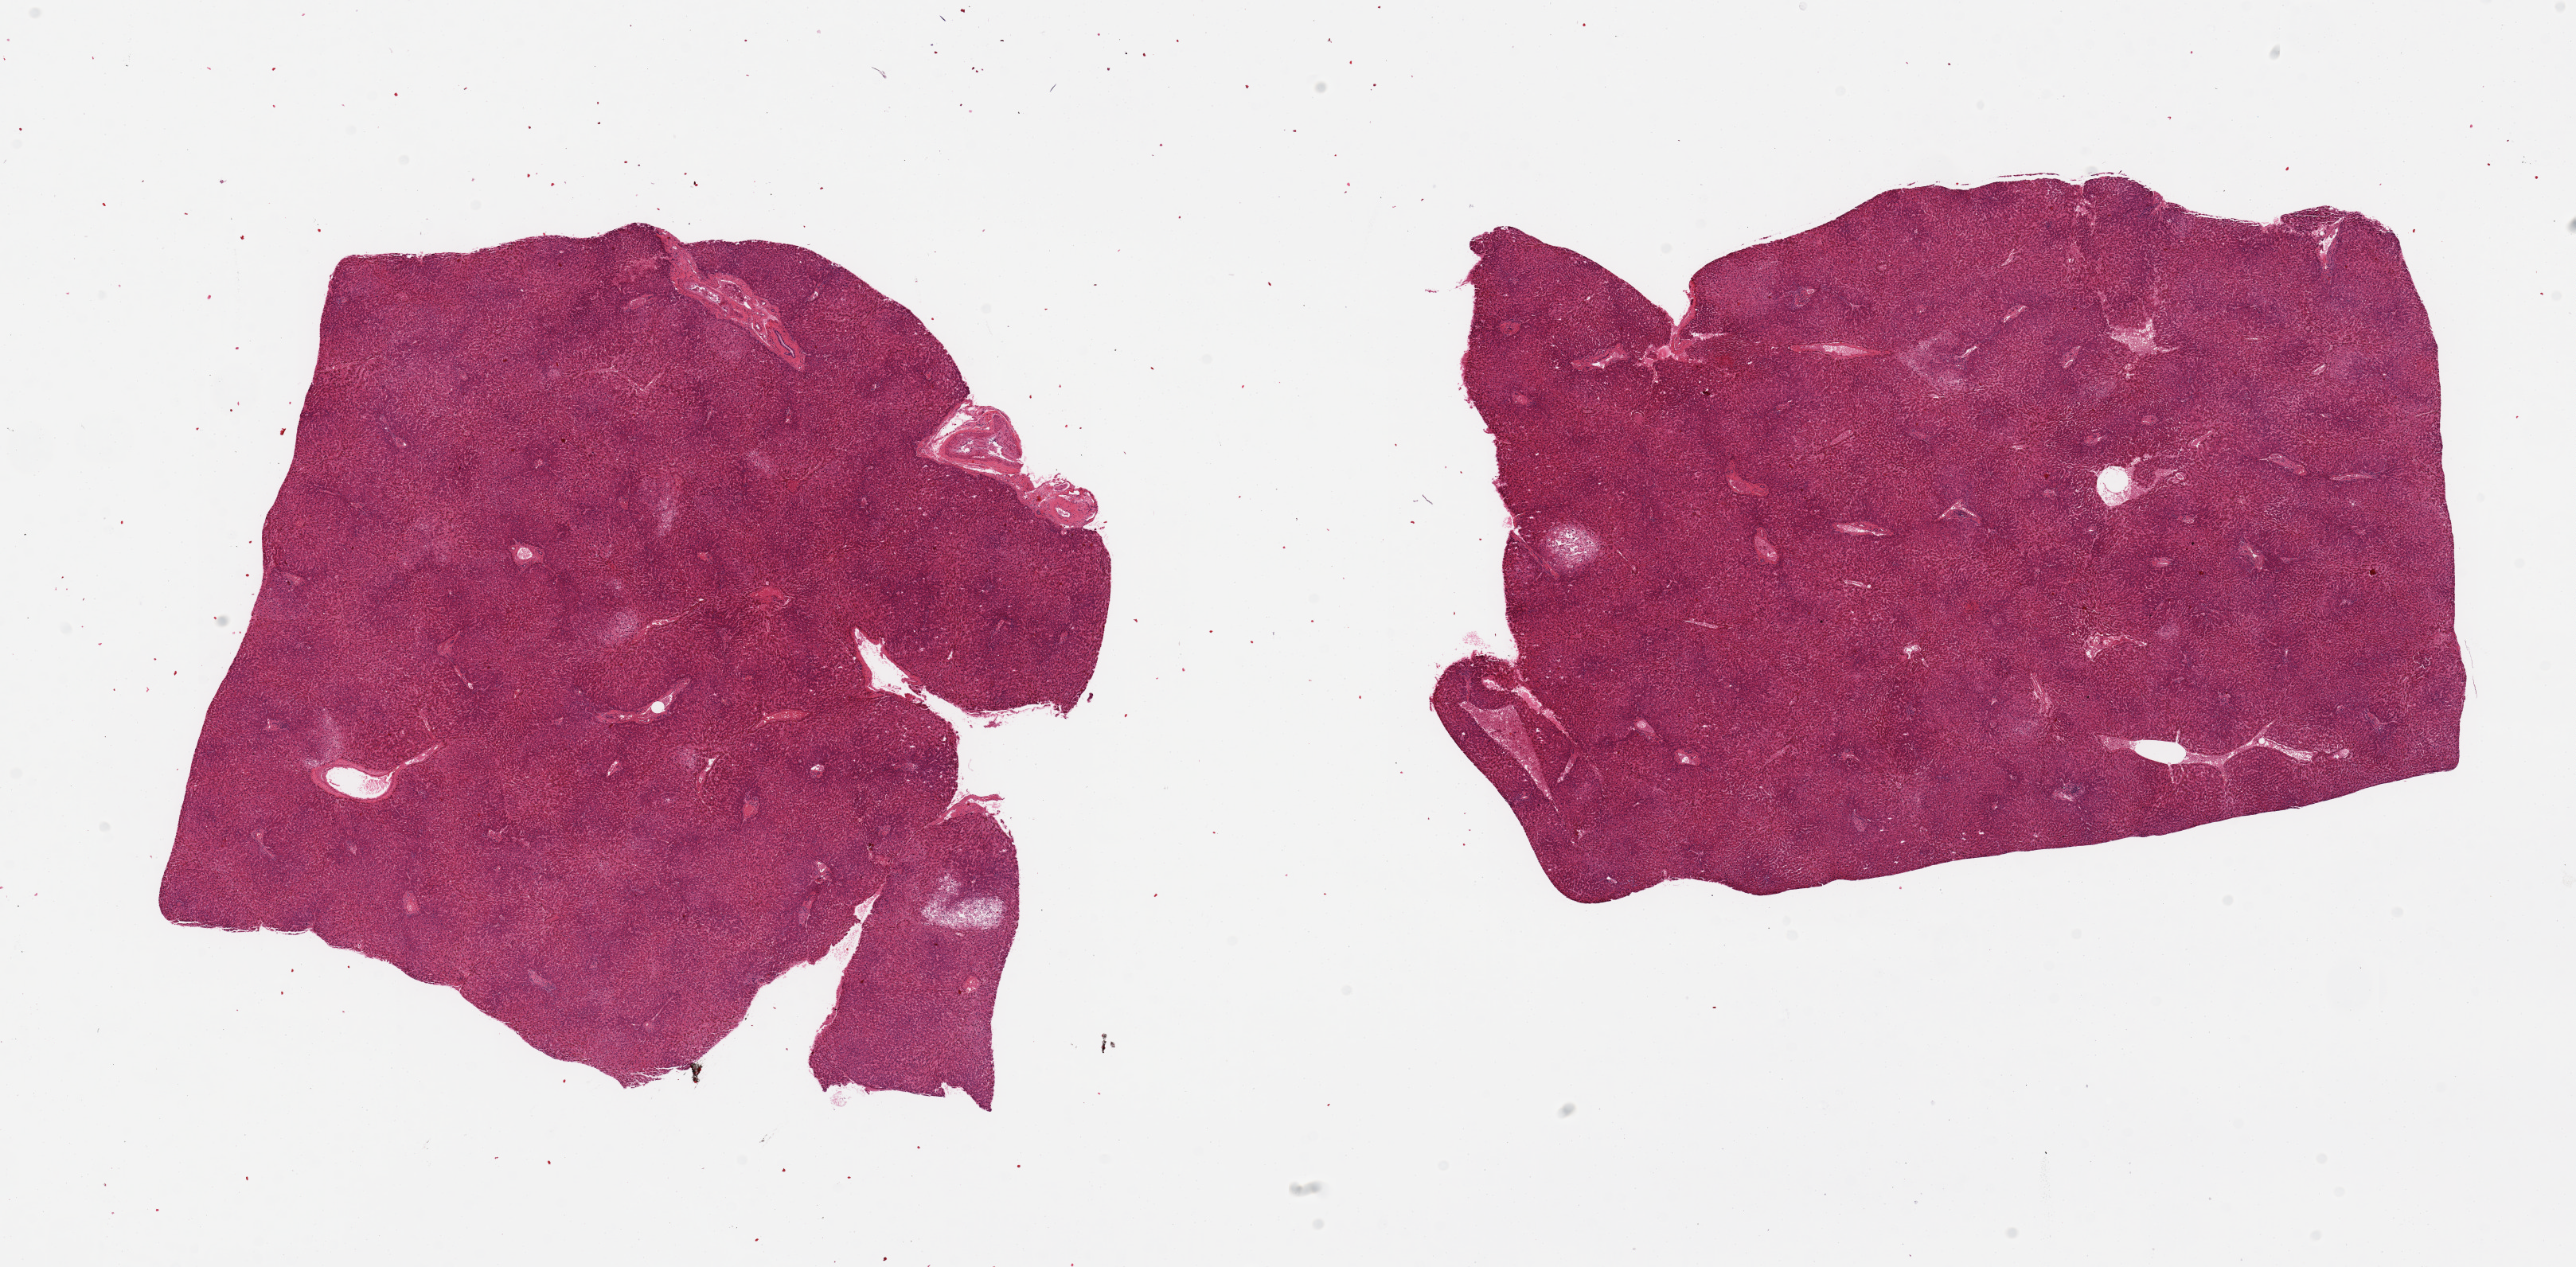
Whole-slide image, hematoxylin and eosin (H&E) stain, brightfield, a low-resolution overview of the entire scanned area, about 25.6 x 12.6 mm (slide scanned at 20x). PAXgene-fixed, paraffin-embedded tissue. Sampled site (target tissue): liver. Donor tissue sample. Male donor.
* reviewer comment on this tissue sample: 2 pieces, foci of hepatocyte necrosis and ballooning degeneration